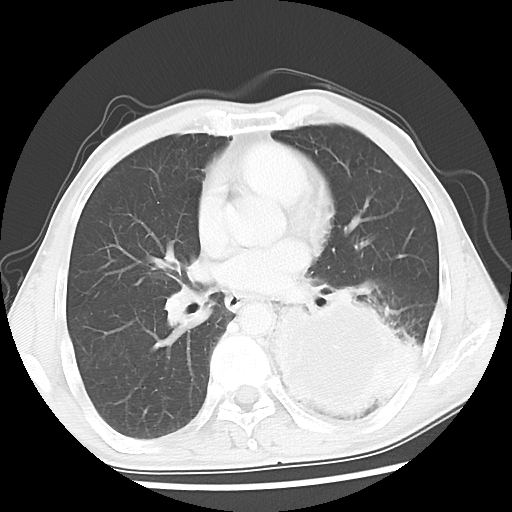
Chest CT, one axial slice; slice 24 of 52 in the series (ordered by position); reconstruction kernel LUNG; lung window (W 1500 / L -600 HU); 5 mm slice thickness; 512 × 512 image matrix, field of view 318 × 318 mm. Male patient, age 60 years. Case-level facts recorded for this patient, not image findings: clinical TNM (as recorded): T4 N0 M0.
Structures marked on this image (rectangle marked by the reading radiologist):
- lung tumour (recorded histology: squamous cell carcinoma): bounding box (x1, y1, x2, y2) in pixels: (268, 286, 423, 424)